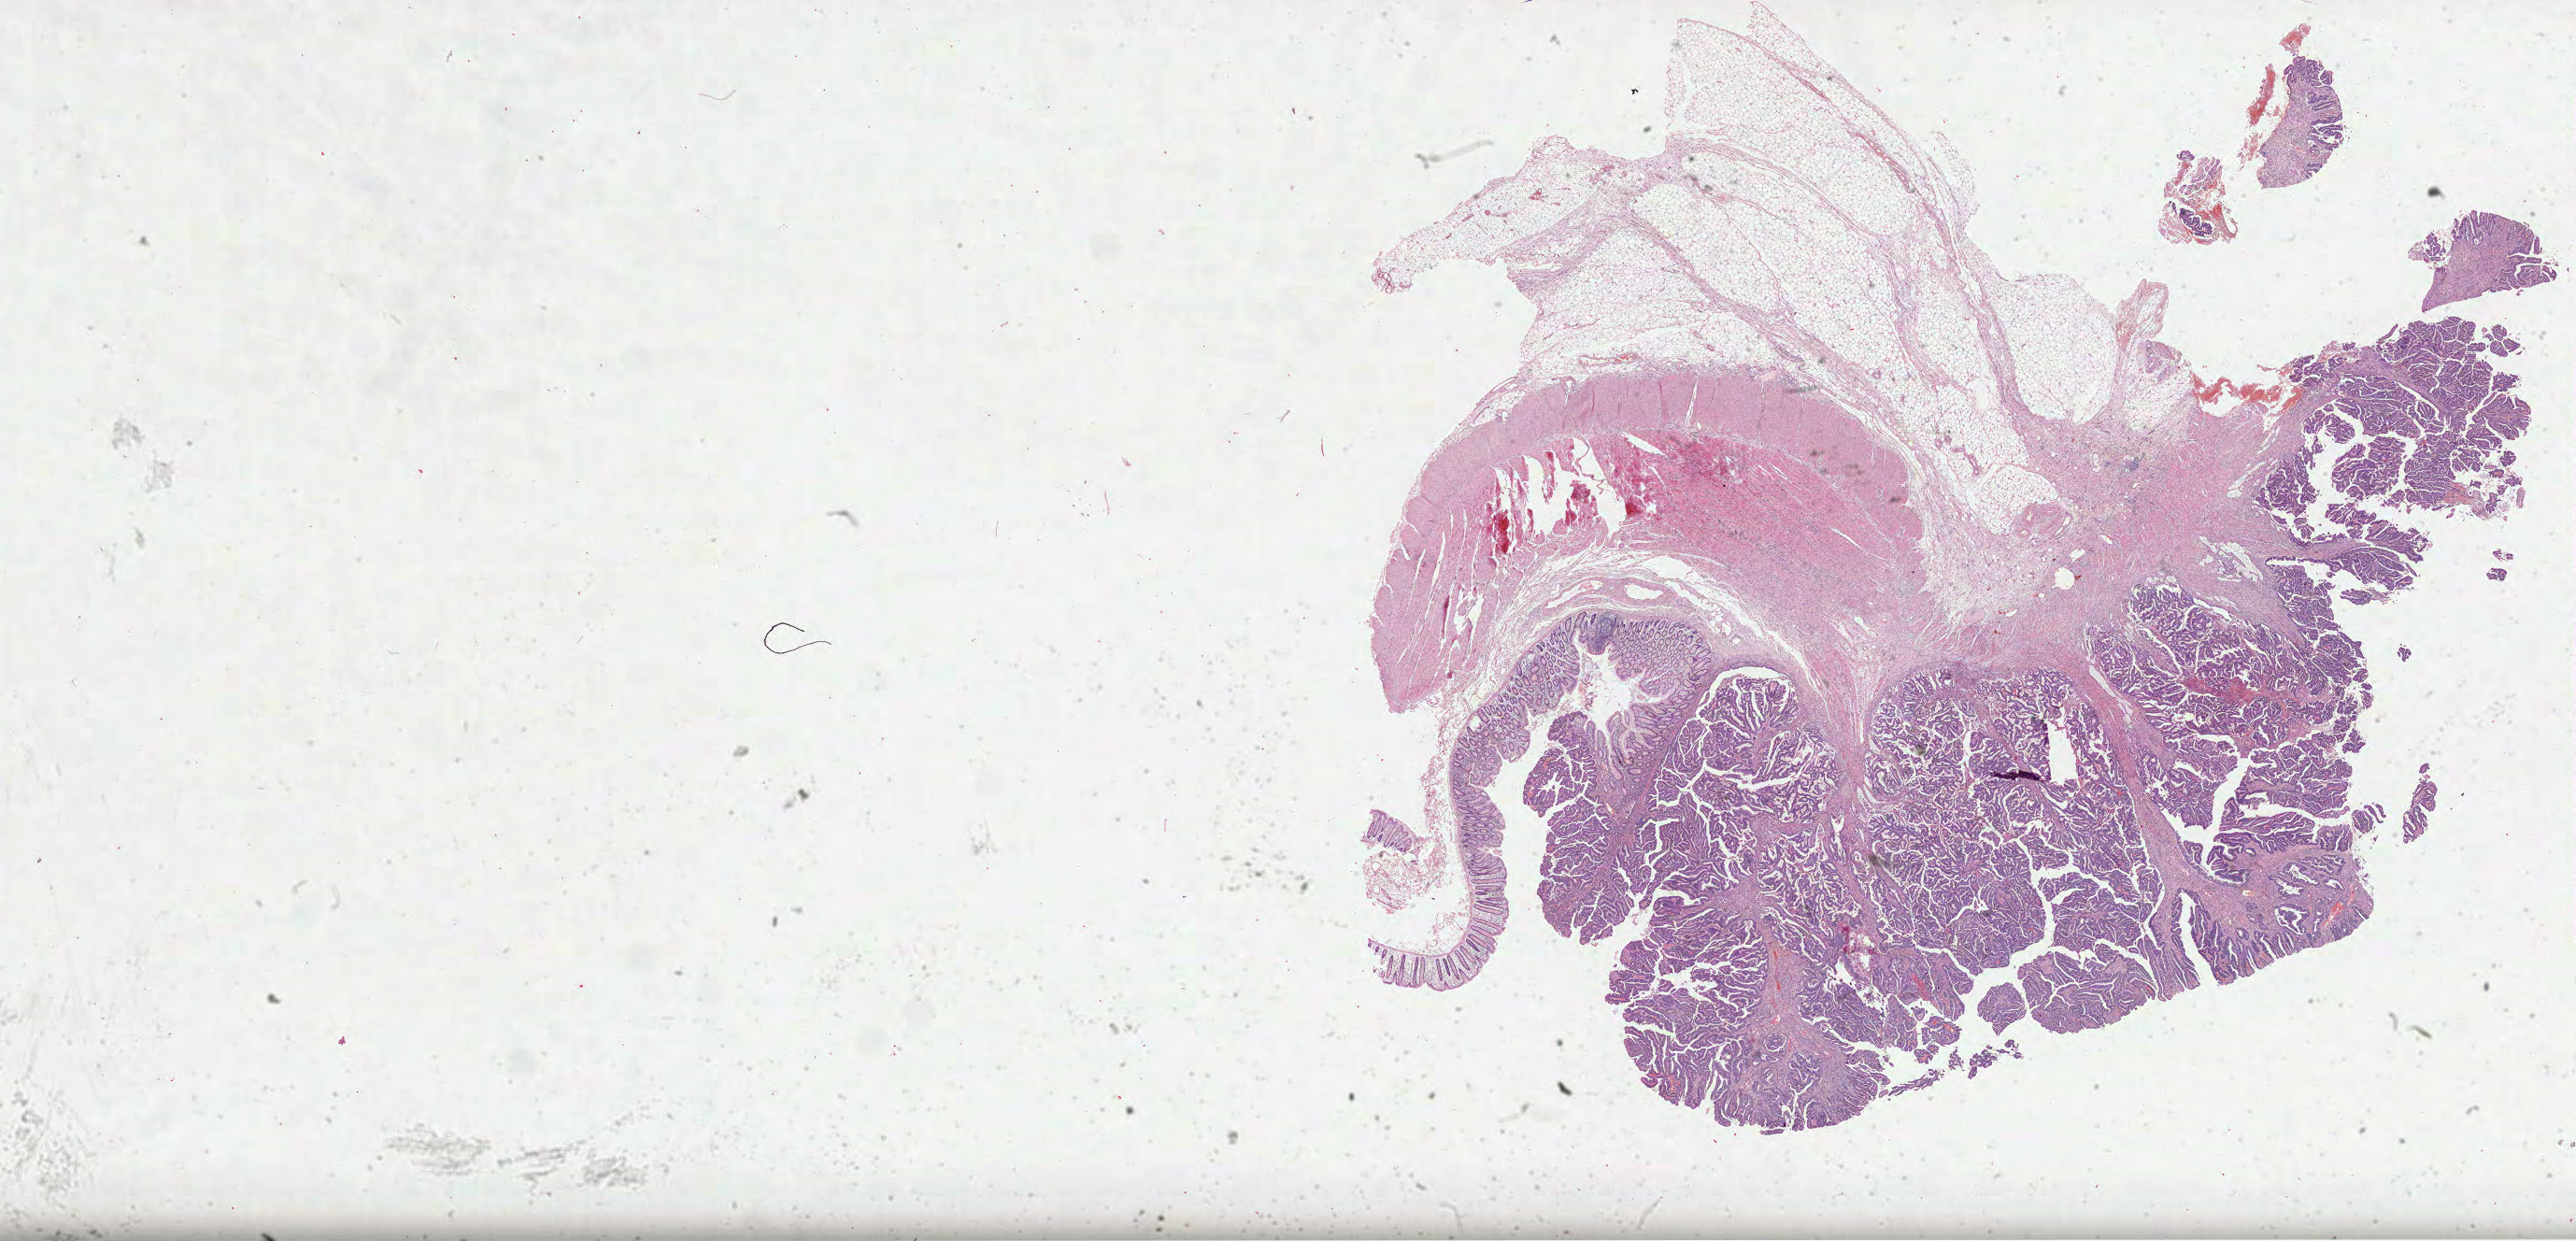
Digitized Hematoxylin and eosin (H&E) stained tissue section (whole slide) — a low-resolution overview of the entire scanned area, about 44.5 x 21.4 mm (from a 40x scan). FFPE section. Colon, primary tumour sample. Patient: male, age at initial diagnosis 64 years.
- diagnosis: Adenocarcinoma, NOS (transverse colon)
- AJCC pathologic stage: IIIB